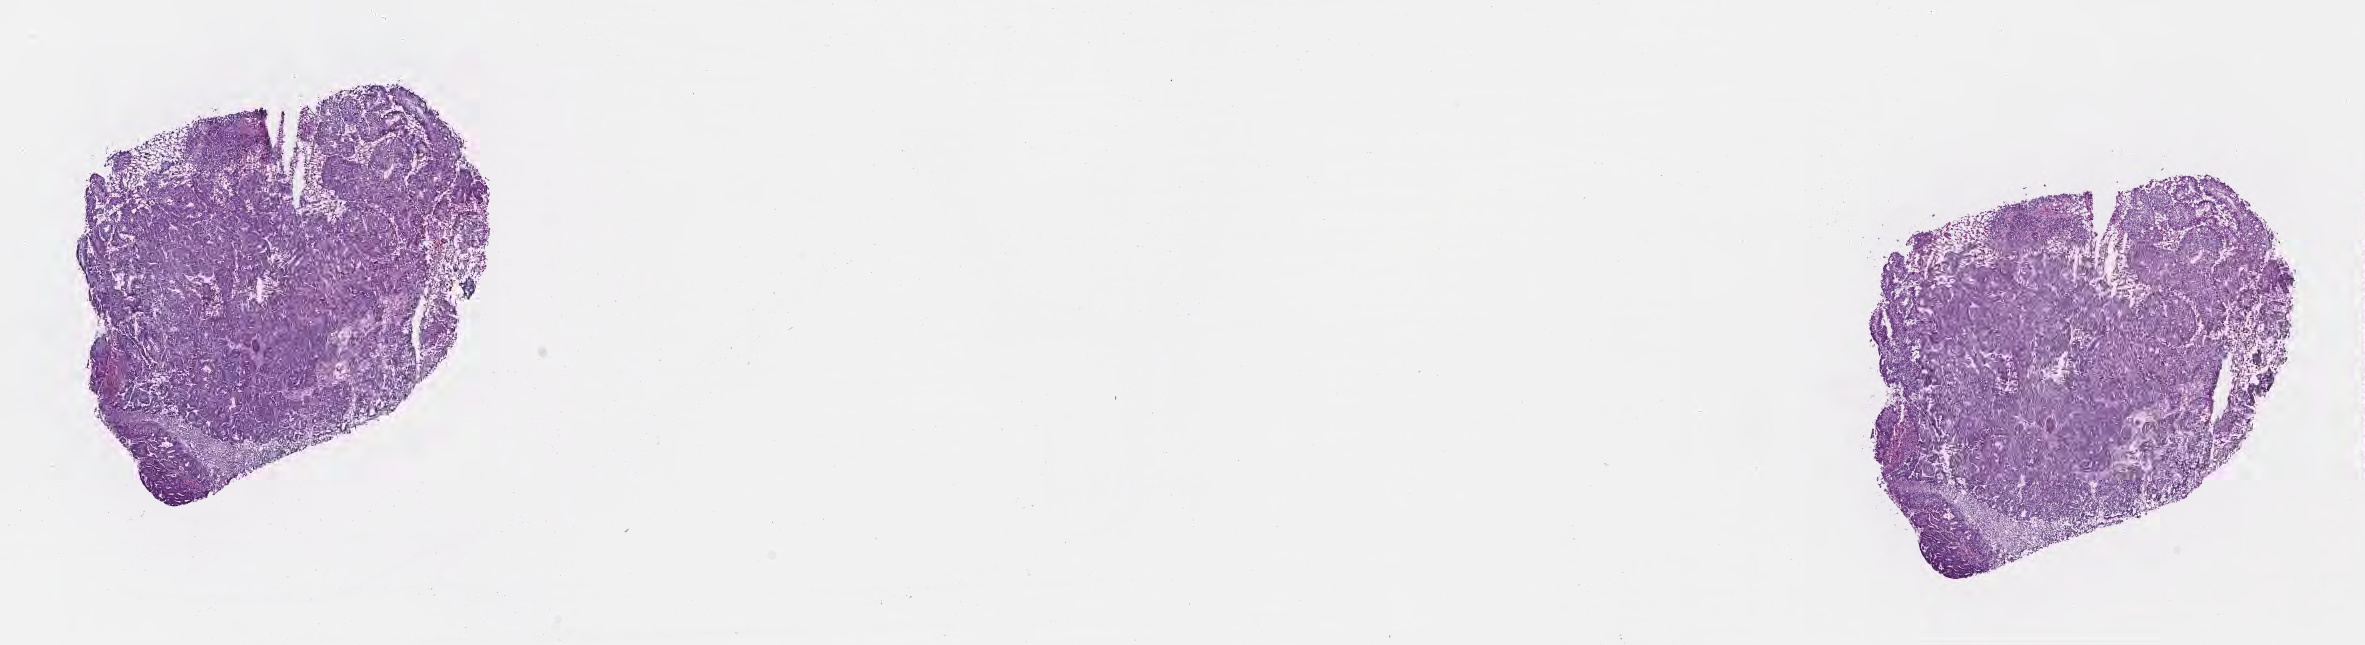
Haematoxylin and eosin whole-slide image — shown as a low-resolution overview of the whole scanned area (about 19.1 x 5.2 mm). Frozen section (tissue freezing medium). Specimen: metastatic tumor tissue, resected from brain. Male patient; age at initial diagnosis 60 years. Pathologist review of this section (percent, as recorded): tumor cells 92%, tumor nuclei 98%, stromal cells 0%, necrosis 8%, normal cells 0%. Infiltration values recorded for this section: lymphocyte infiltration 0%, monocyte infiltration 0%, neutrophil infiltration 0%.
Patient diagnosis (primary): Adenocarcinoma, NOS. Section: bottom of the tissue portion.